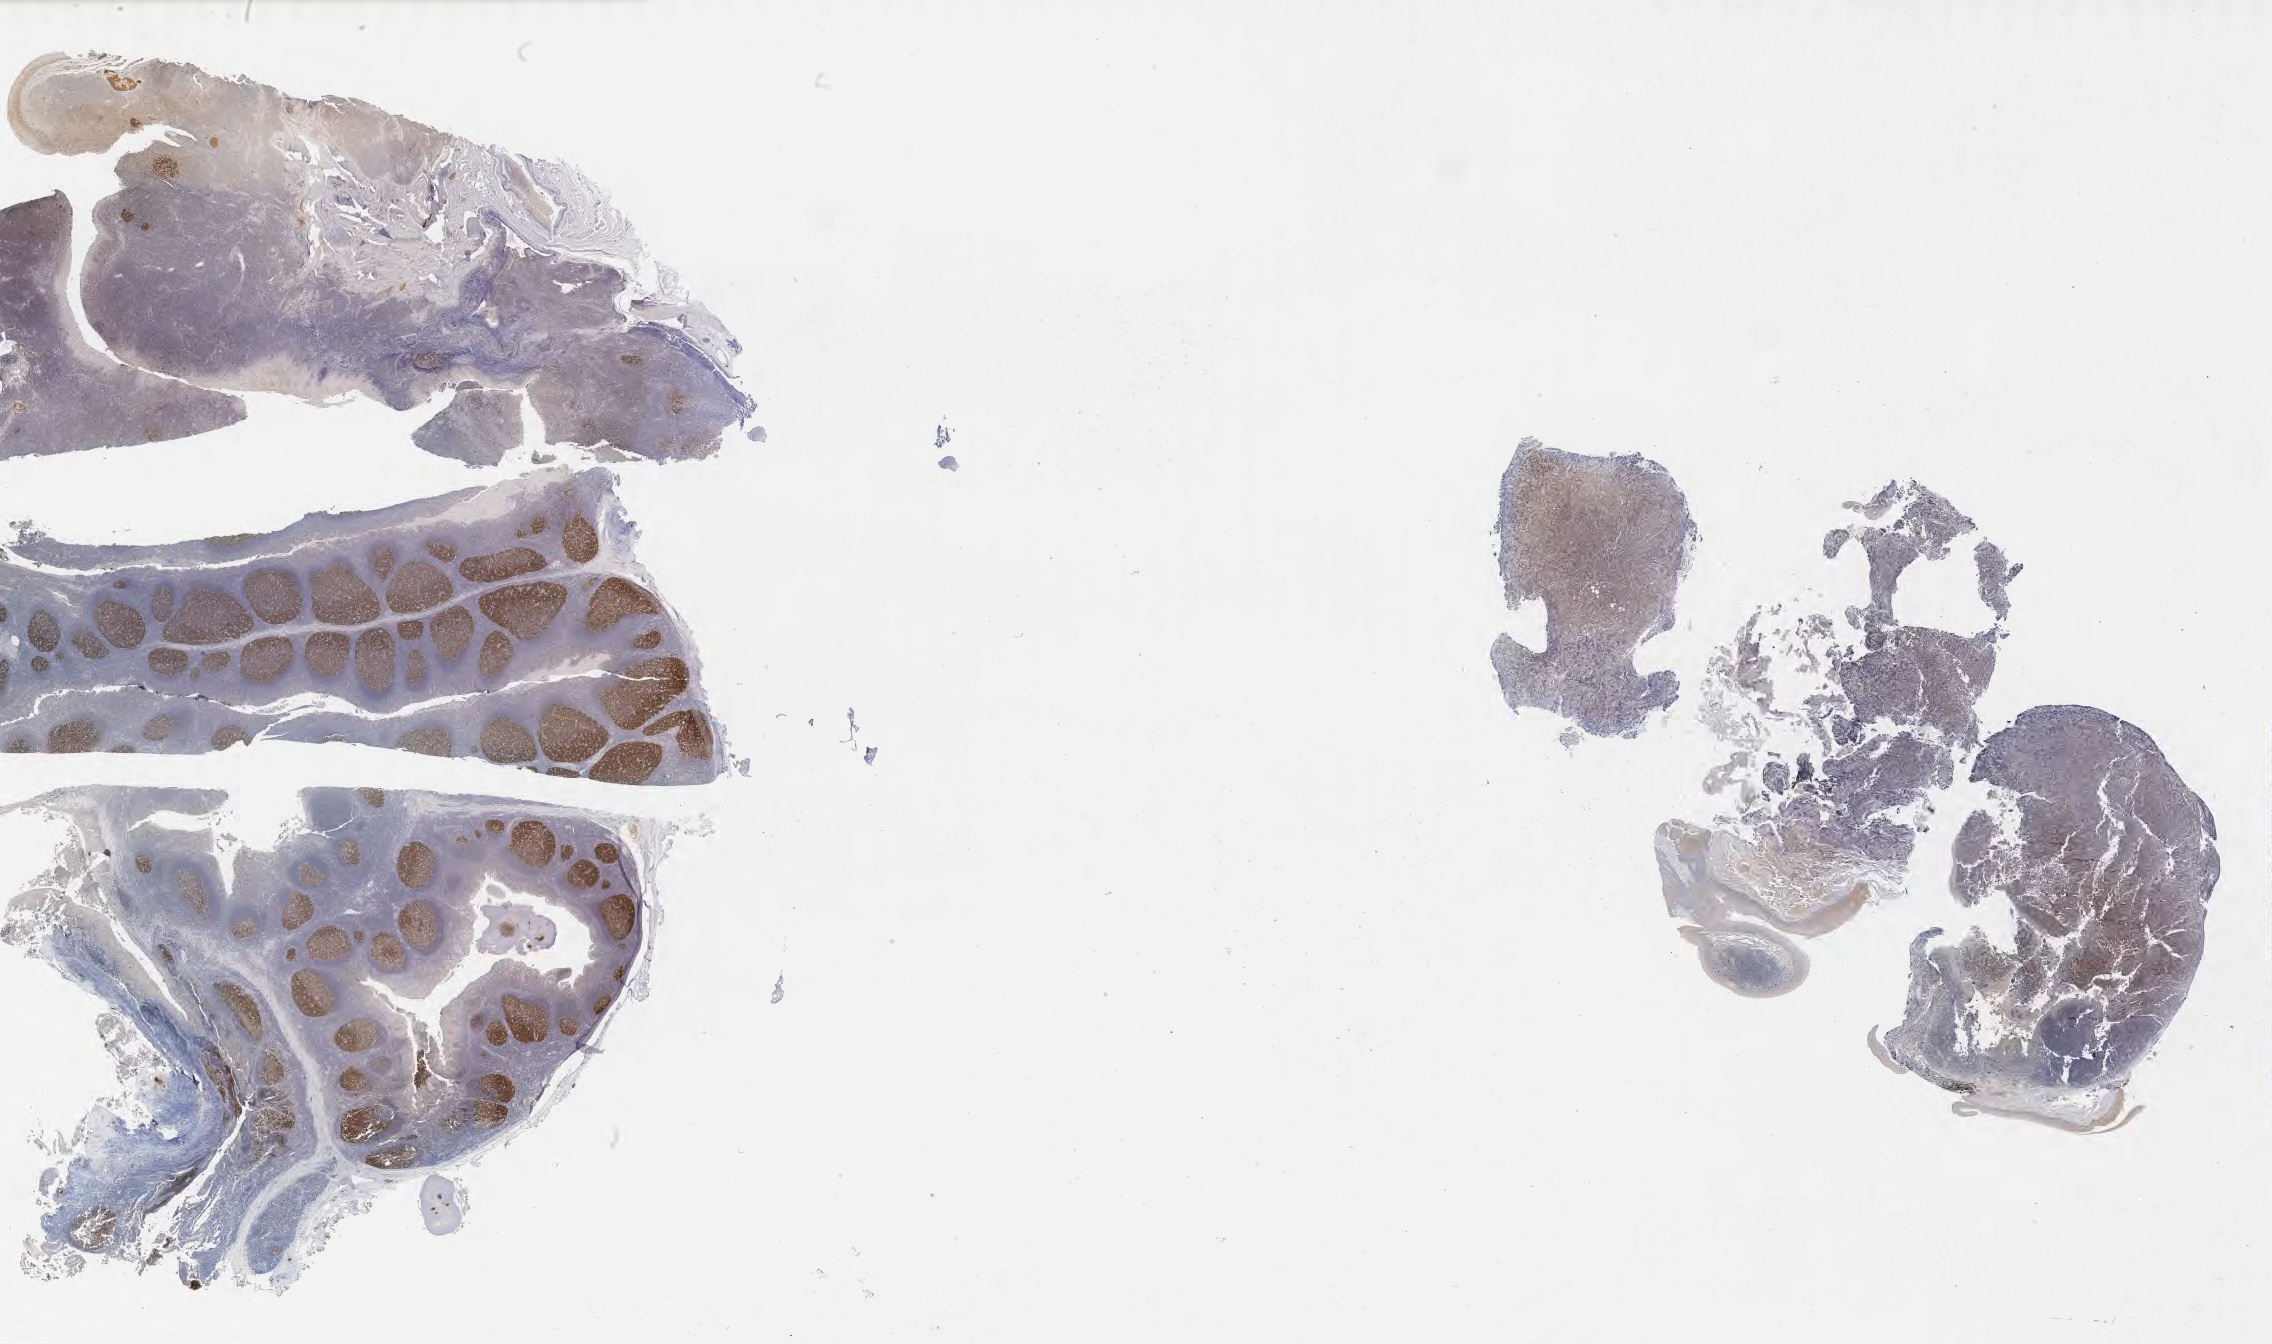
IHC for BCL6, whole-slide image — low-resolution overview of the scanned area, about 36.7 x 21.7 mm. Tumor tissue. Patient: male, age 63 years.
Histologic diagnosis: Burkitt lymphoma, NOS.